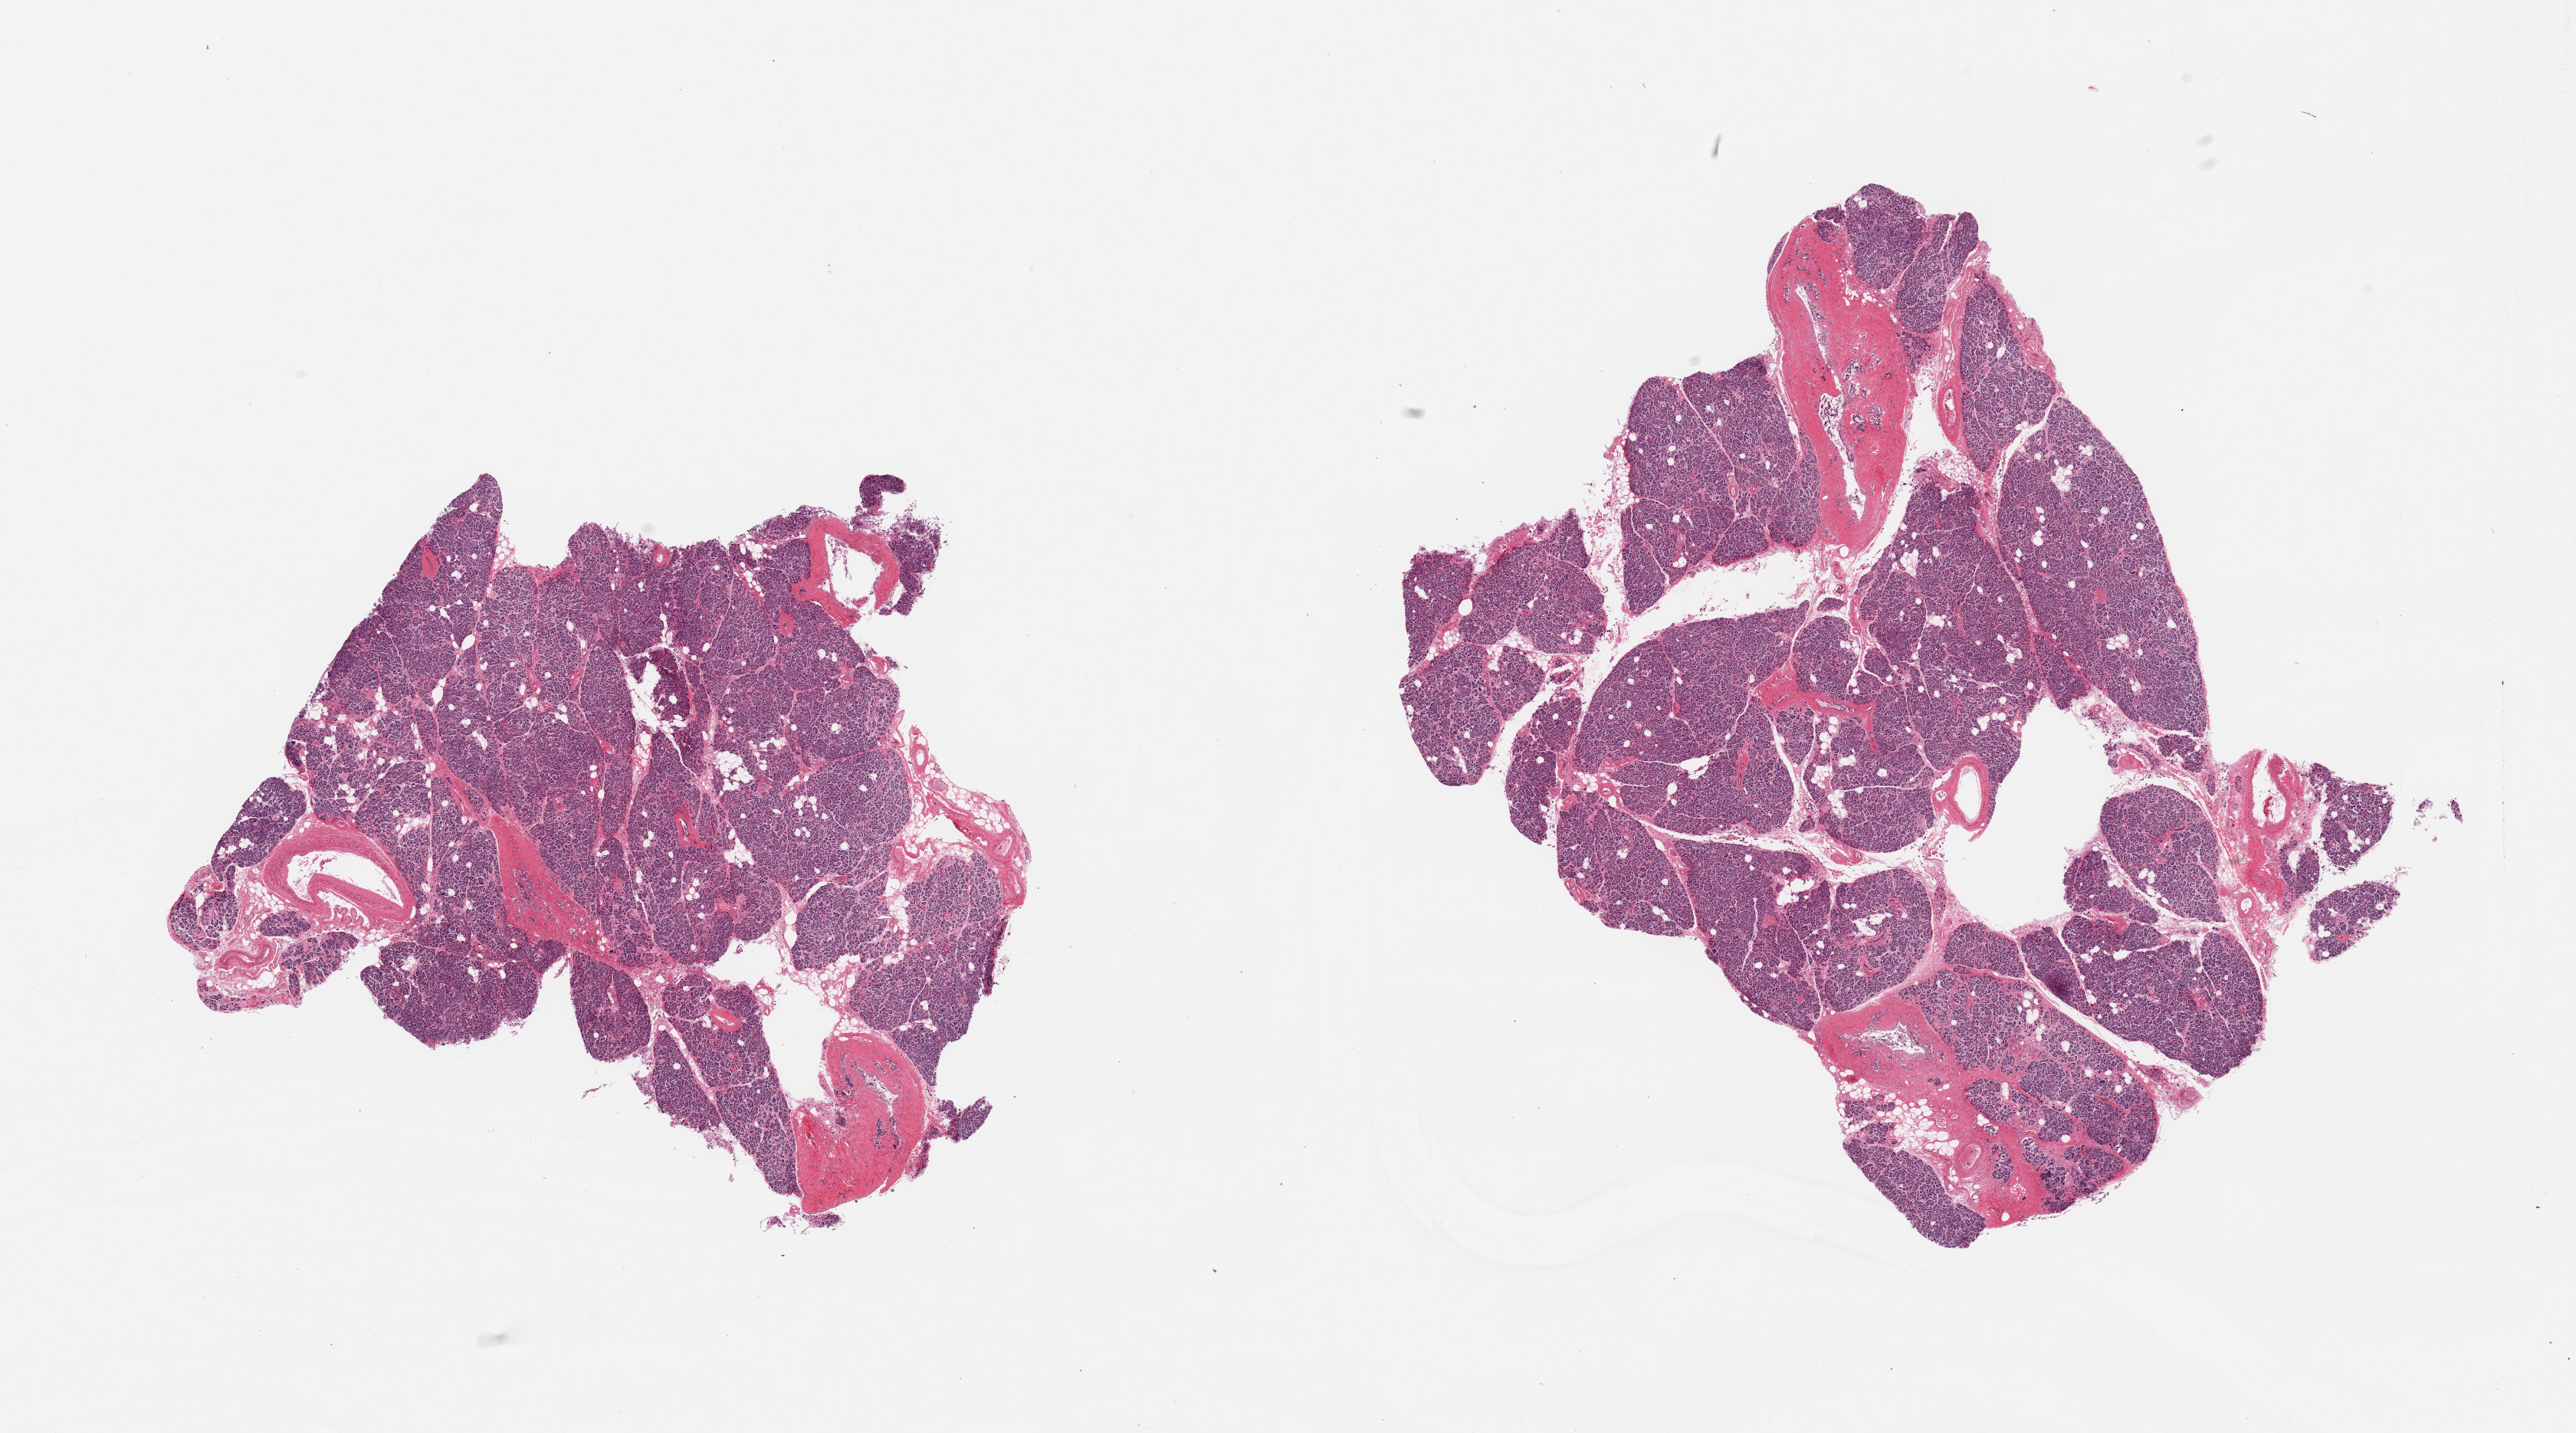
Haematoxylin and eosin whole-slide image, brightfield — low-resolution overview of the scanned area, about 26.6 x 14.8 mm (slide scanned at 20x). PAXgene-fixed, paraffin-embedded tissue. Sampled site (target tissue): pancreas. Tissue donor sample.
Pathologist's review note for this sample: 2 pieces; mild fibrosis and focal atrophy, ductal epithelium sloughing.